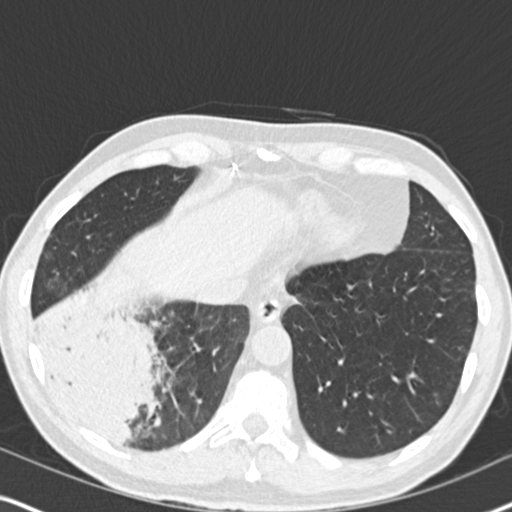
Axial slice from a low-dose chest CT screening exam; second screening round (one year after baseline); lung window (W 1500 / L -600 HU); 2 mm slice thickness; slice 125 of 182 in the series; 512 × 512 image matrix, field of view 330 × 330 mm. Male participant, aged 61 years at enrolment.
Lesion marked by an expert reader, bounding box (x1, y1, x2, y2) in pixels: (27, 292, 182, 457). Reader record for this screening exam (exam-level; its link to the box is not recorded): non-calcified nodule or mass ≥4 mm, right lower lobe, 90 × 80 mm, soft tissue attenuation, pre-existing on the prior screen: yes; interval growth: yes.